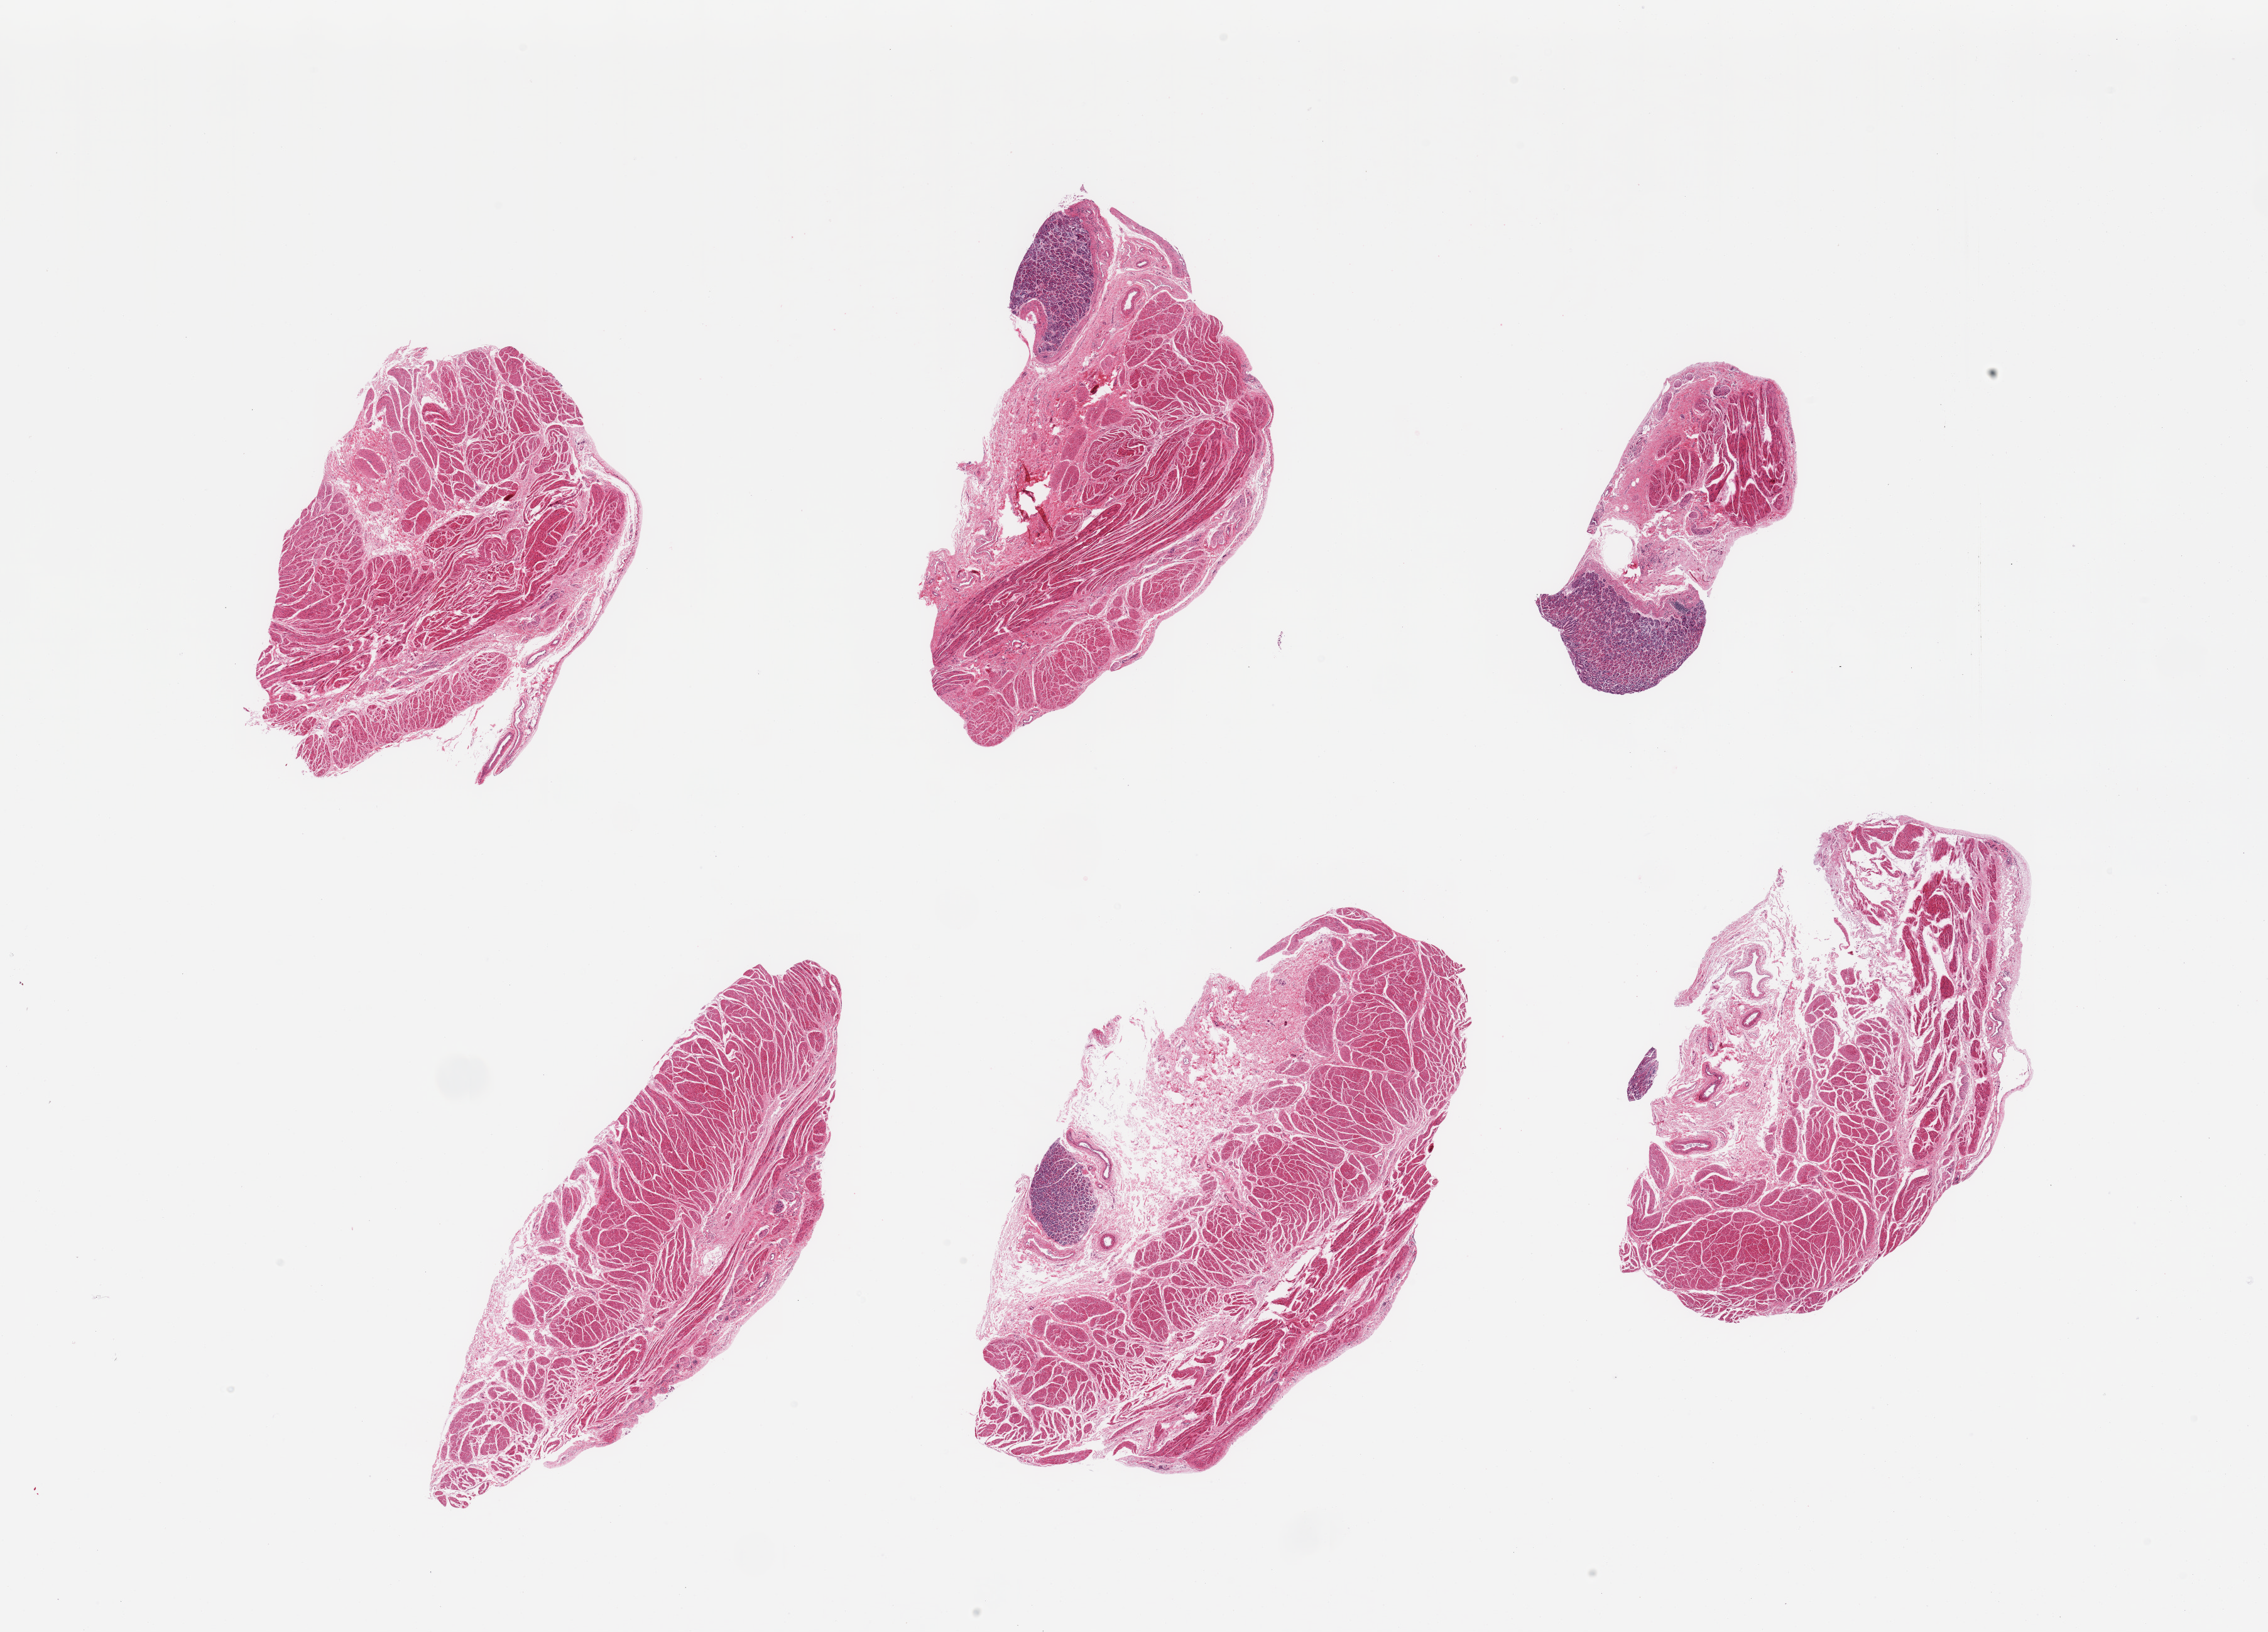
Digitized hematoxylin and eosin (H&E)-stained section — low-resolution overview of the scanned area, about 28.5 x 20.5 mm (slide scanned at 20x). PAXgene-fixed paraffin-embedded (PFPE) section. Sampled site (target tissue): gastroesophageal junction. Donor tissue sample. Female donor.
Reviewer comment on this tissue sample: 6 pieces, confirmed target muscularis, few ~1mm nubbins of adherent cardiac mucosa.